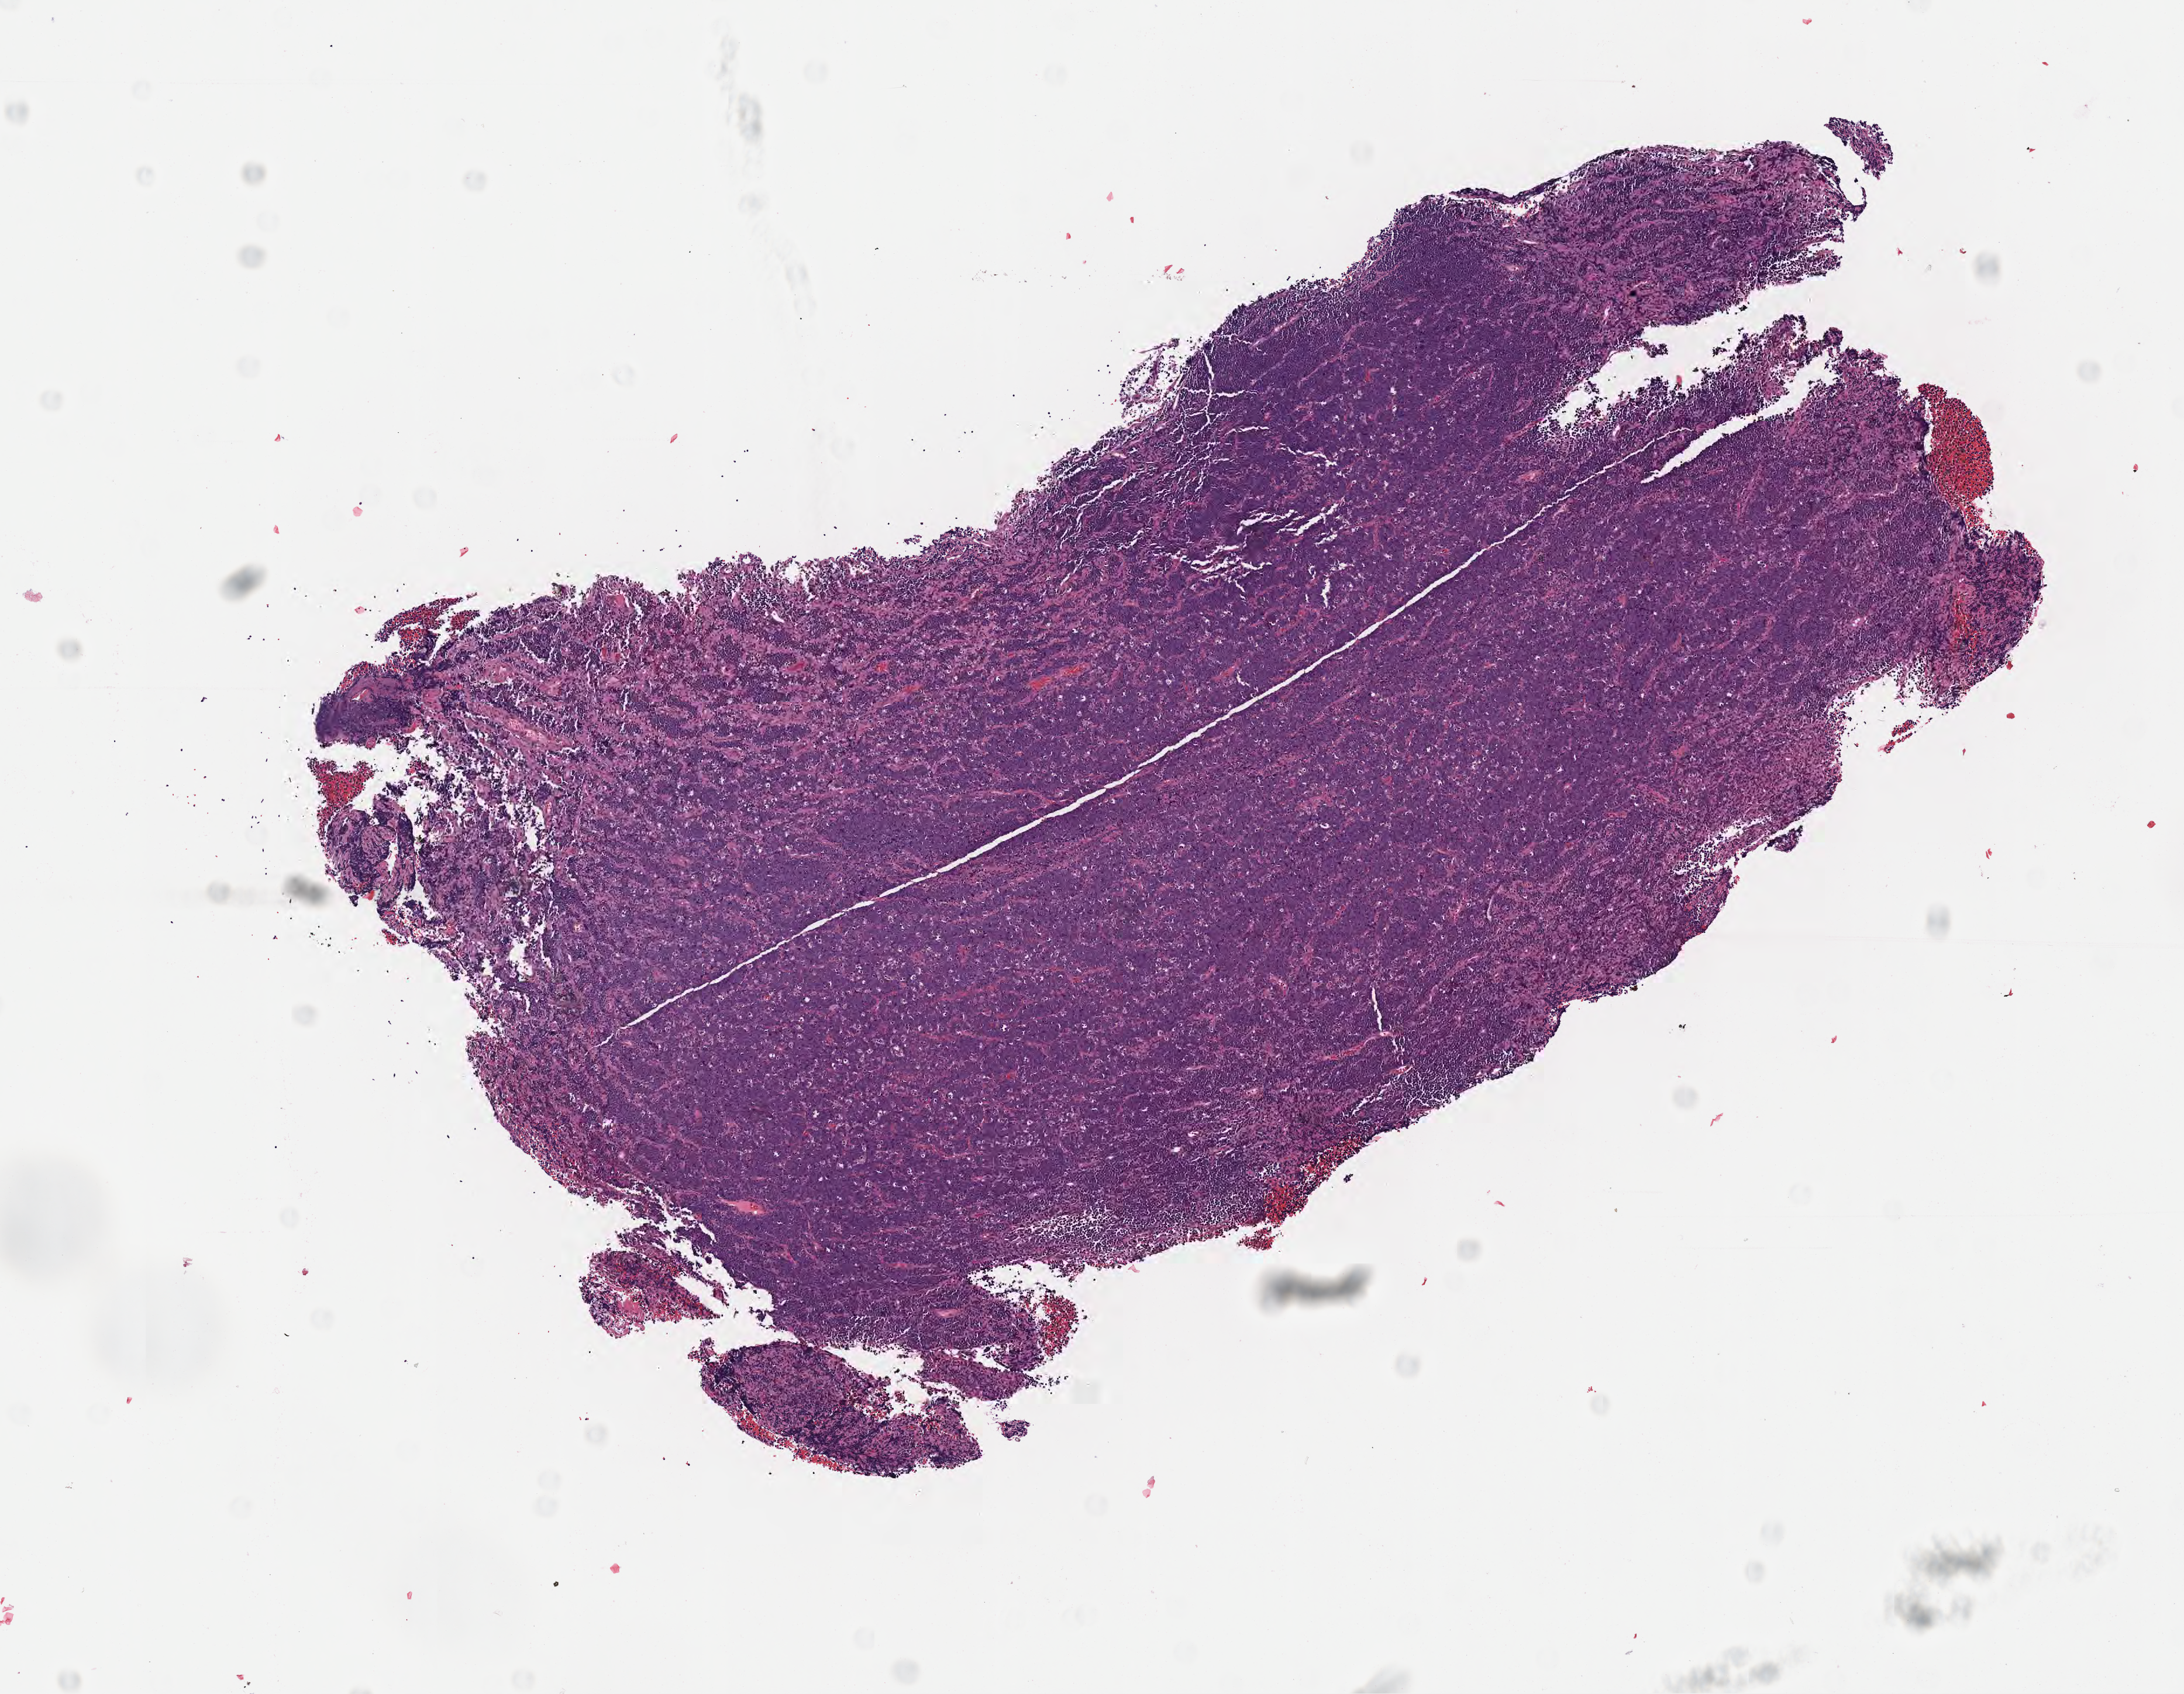
H&E whole-slide image — whole scanned area (about 7.6 x 5.9 mm) shown as a low-resolution overview; specimen: tumor tissue; anatomic site: cranium. Male patient, age 11 years.
Diagnosis: Diffuse large B-cell lymphoma, NOS.